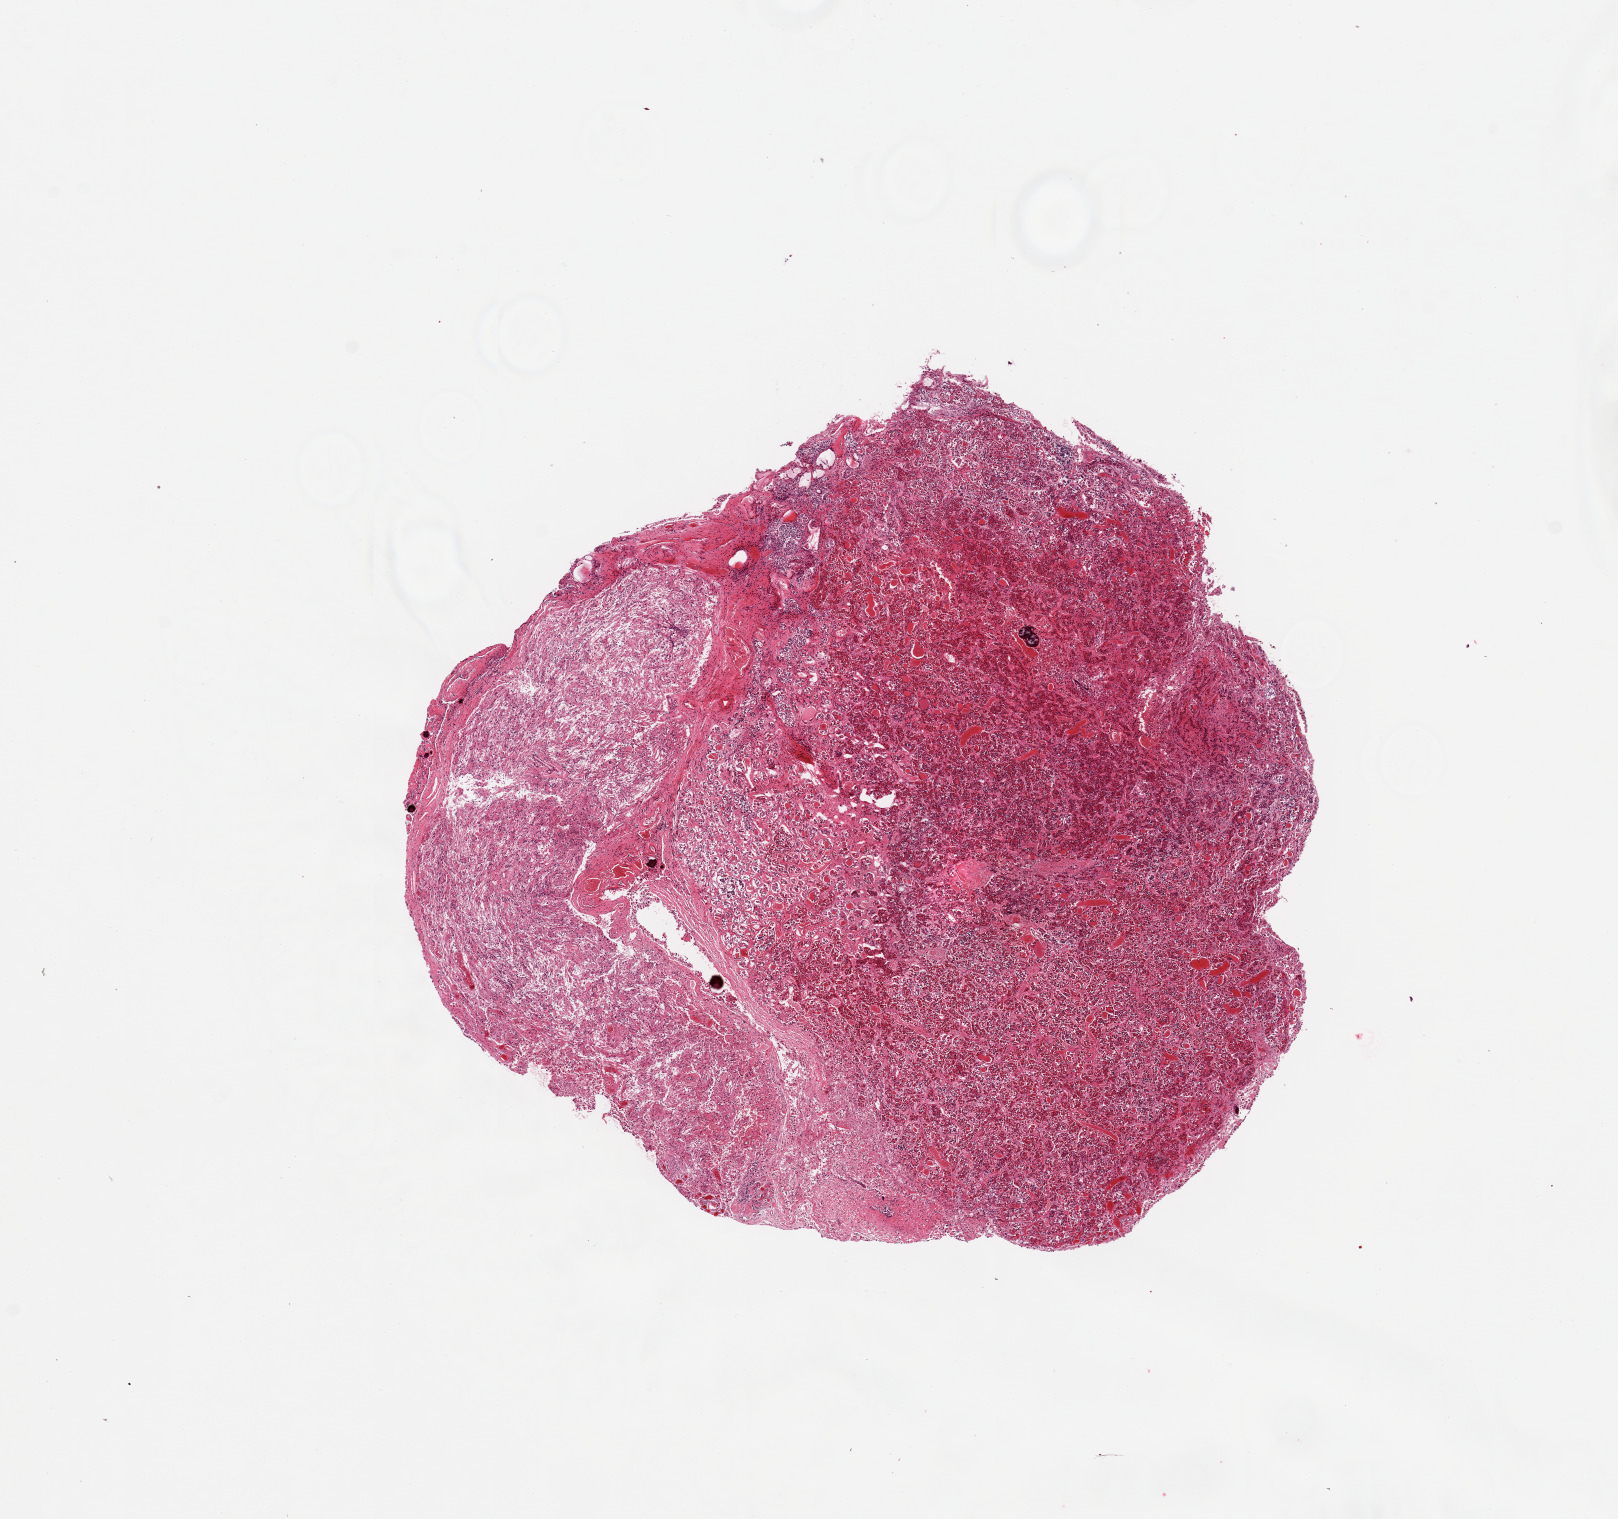
Whole-slide image, haematoxylin and eosin stain, brightfield — a low-resolution overview of the entire scanned area, about 12.8 x 12.0 mm. PAXgene-fixed paraffin-embedded (PFPE) section. Section of pituitary (target tissue). Tissue donor sample. Female donor.
Pathologist's review note for this sample: 1 piece; anterior and posterior.